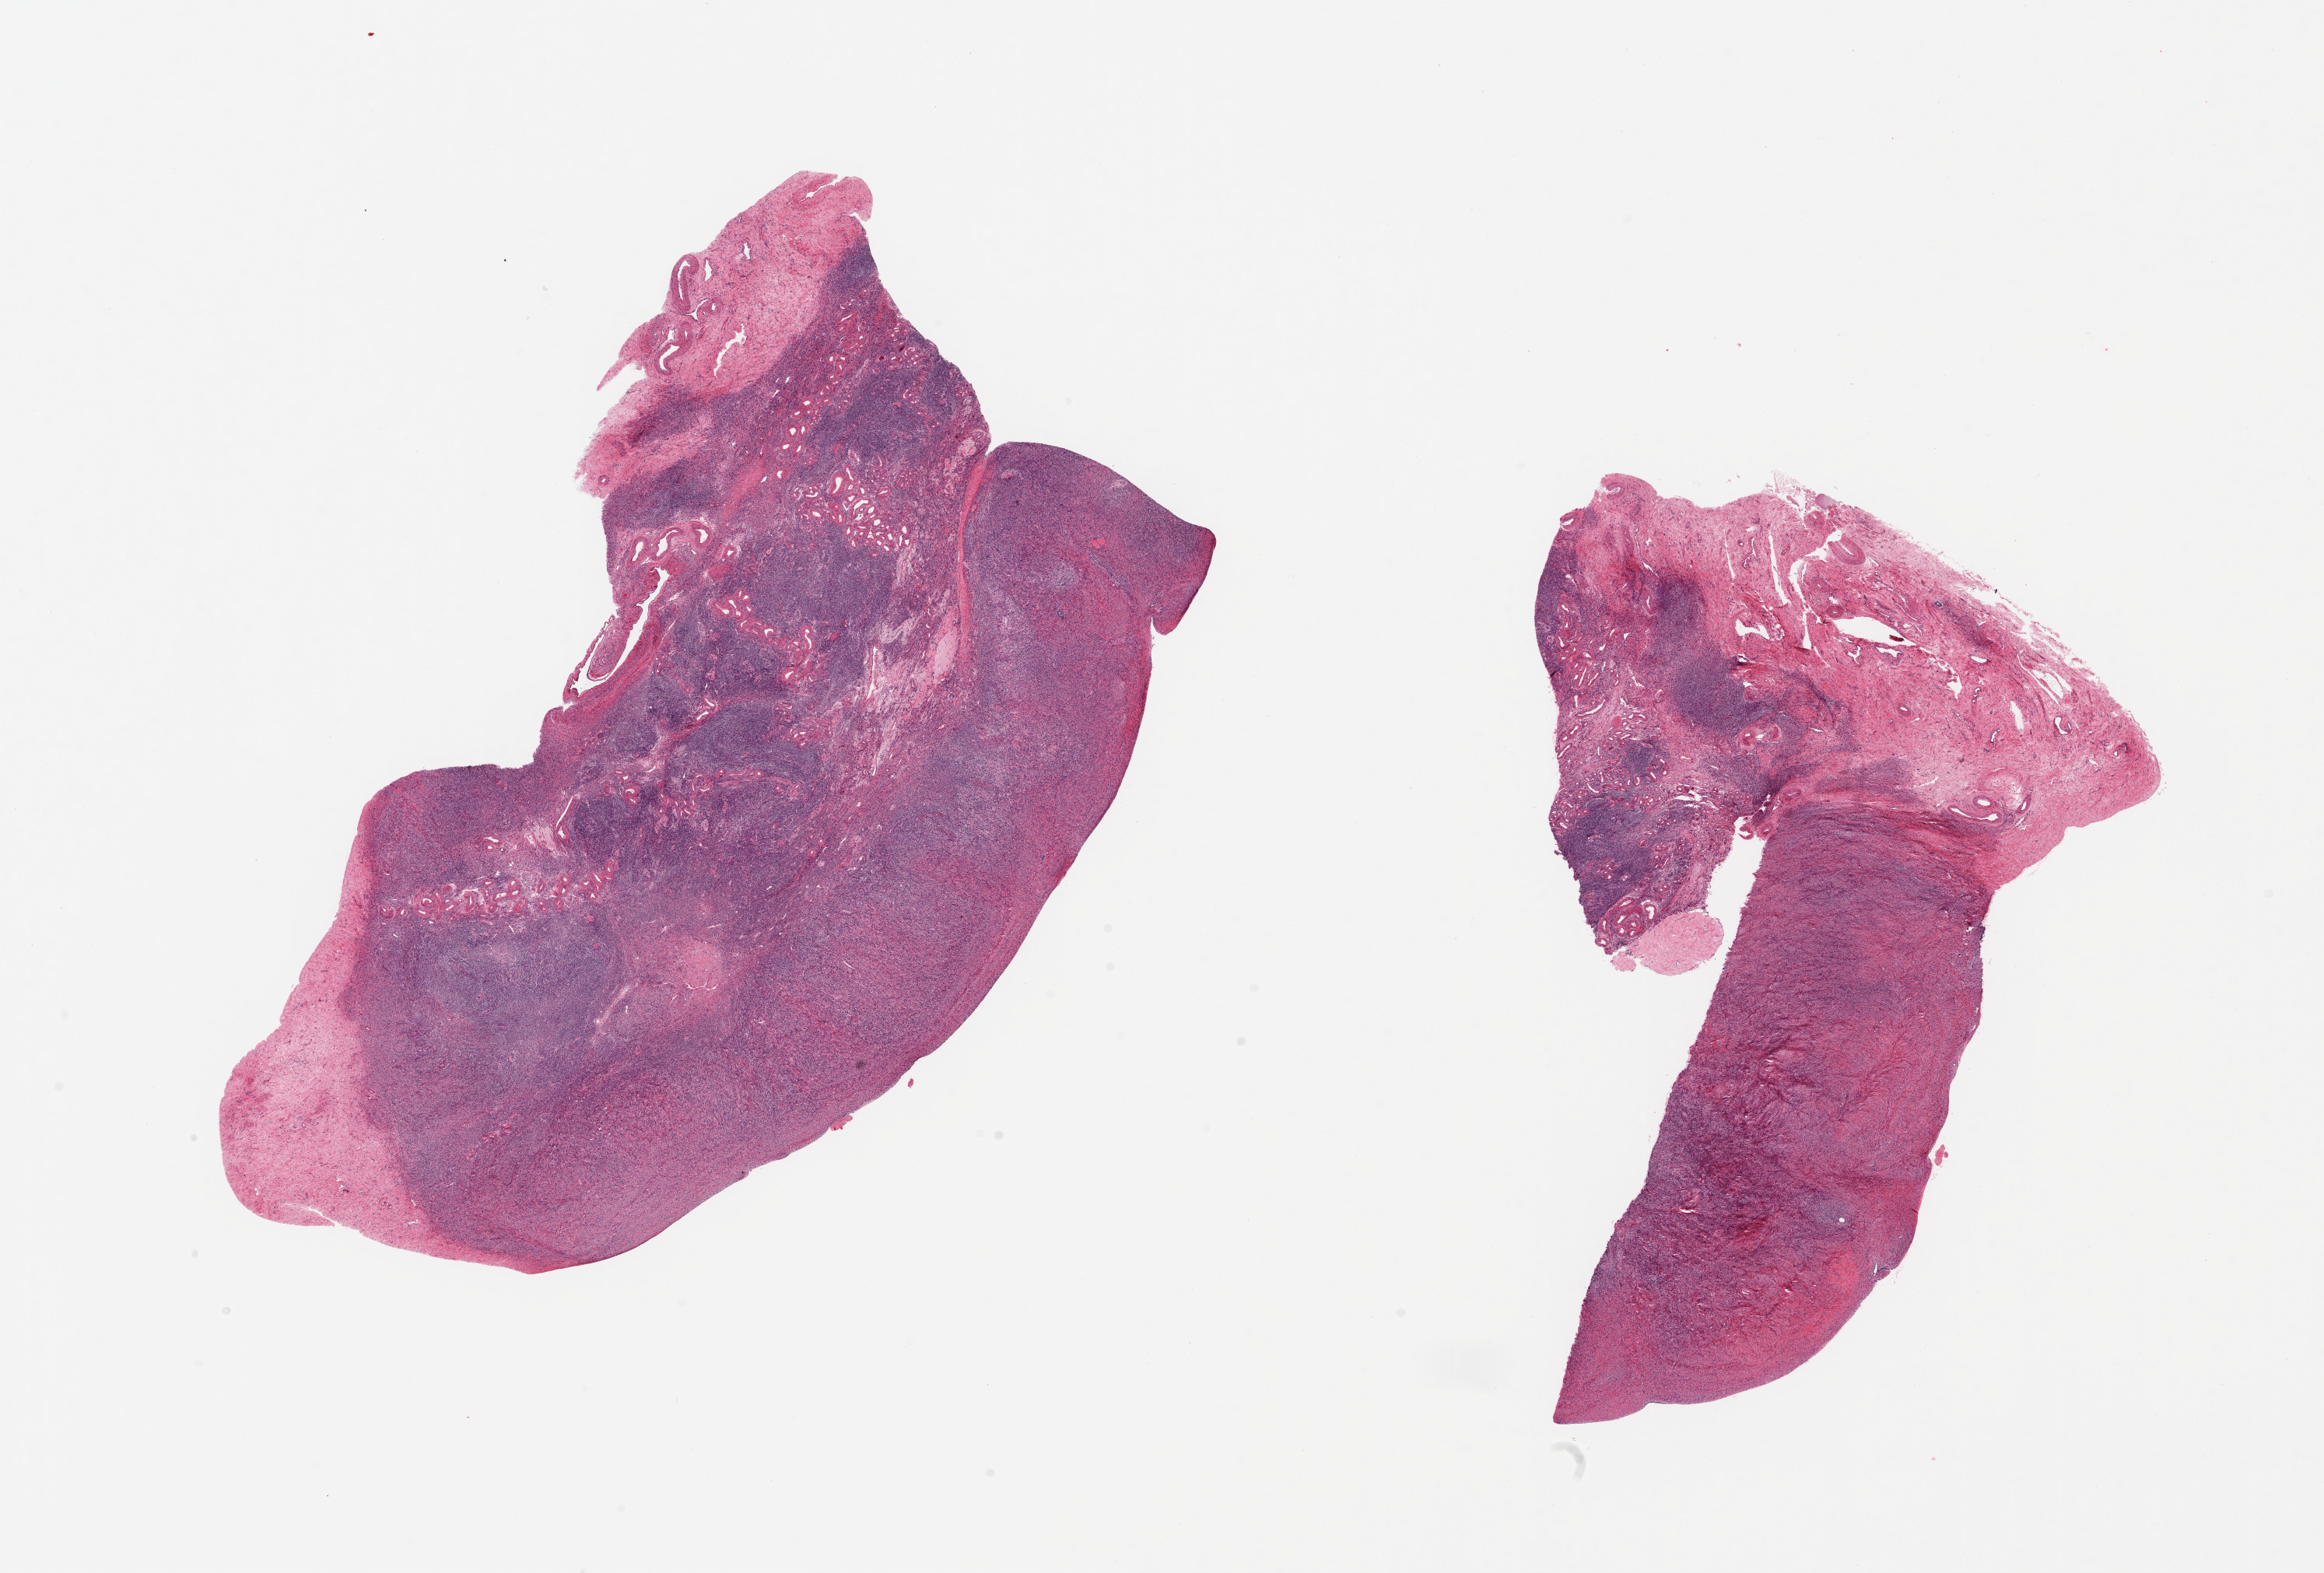
H&E whole-slide image, brightfield — whole scanned area (about 23.6 x 16.0 mm) shown as a low-resolution overview. PAXgene-fixed, paraffin-embedded tissue. Sampled site (target tissue): ovary. Donor tissue sample. Female donor.
Pathologist's review note for this sample: 2 pieces; 20 & 40% external fibrovascular stroma.